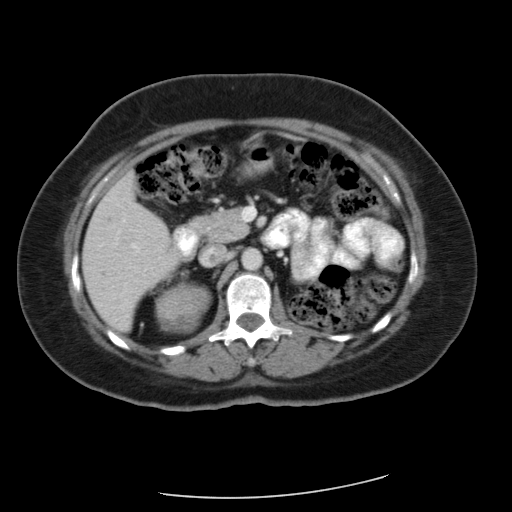
Contrast-enhanced abdominal CT, one axial slice. Slice 32 of 56 in the series (ordered by position). Reconstruction kernel FC12. Soft-tissue window (W 400 / L 40 HU). 512 × 512 image matrix. Patient: female, 58 years. From the clinical record (not read from this slice): diagnosis: adrenocortical carcinoma; tumour side: right adrenal; tumour size at pathology: 9 cm.
Outlined on this slice (semi-automatically segmented with operator editing):
- mass: bounding box [x1, y1, x2, y2] px = [156, 286, 210, 330]